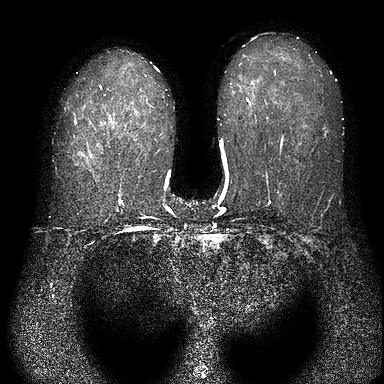
MRI of the breasts; 1 image, one mid-volume slice chosen by position. Patient in her 40s.
Image 1: fluid-sensitive (T2/STIR) axial slice, slice 46 of 90.
Patient-level pathology facts (from the clinical record, not from the images): pathology diagnosis: invasive ductal CA (left breast); receptor status (as recorded): ER pos, PR pos, HER2 pos.